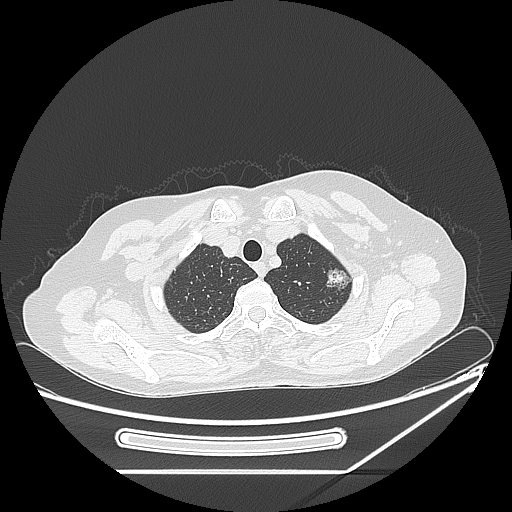
Chest CT, one axial slice; position 210 of 250 along the scan axis; reconstruction kernel LUNG; lung window (W 1500 / L -600 HU); 1.25 mm slice thickness; 512 × 512 image matrix, field of view 409 × 409 mm. Patient: female, 57 years. From the clinical record (not read from this slice): clinical TNM (as recorded): T1c N0 M0; histopathological grade: G2-3.
Outlined on this slice (rectangle marked by the reading radiologist):
- lung tumour (recorded histology: adenocarcinoma): box from (x=323, y=266) to (x=351, y=295) px